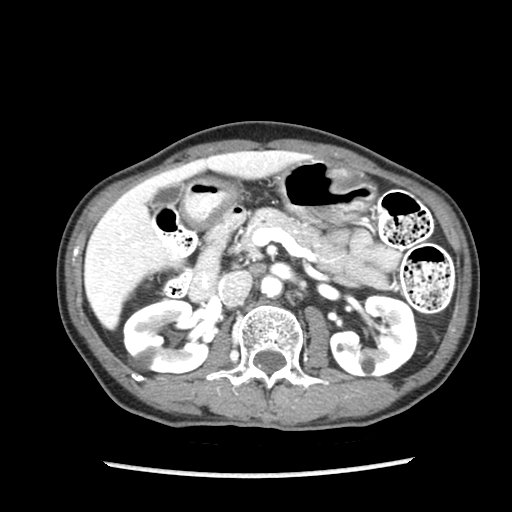
Contrast-enhanced abdominal CT (liver protocol), one axial slice; position 43 of 87 along the scan axis; reconstruction kernel STANDARD; 140 kVp; soft-tissue window (W 400 / L 40 HU); 2.5 mm slice thickness; 512 × 512 image matrix. From the clinical record (not read from this slice): diagnosis: hepatocellular carcinoma (patient treated with transarterial chemoembolisation; whether this scan precedes or follows treatment is not stated here); TNM stage (as recorded): Stage-IIIB; Child-Pugh class: A; tumour nodularity: uninodular.
Structures marked on this image (semi-automatic segmentation, software-assisted and operator-edited):
- liver parenchyma outside the tumour (the mass and vessels are separate outlines, so this box may not span the whole liver): box from (x=84, y=150) to (x=306, y=329) px
- liver vessels: (x=96, y=157)–(x=249, y=305)